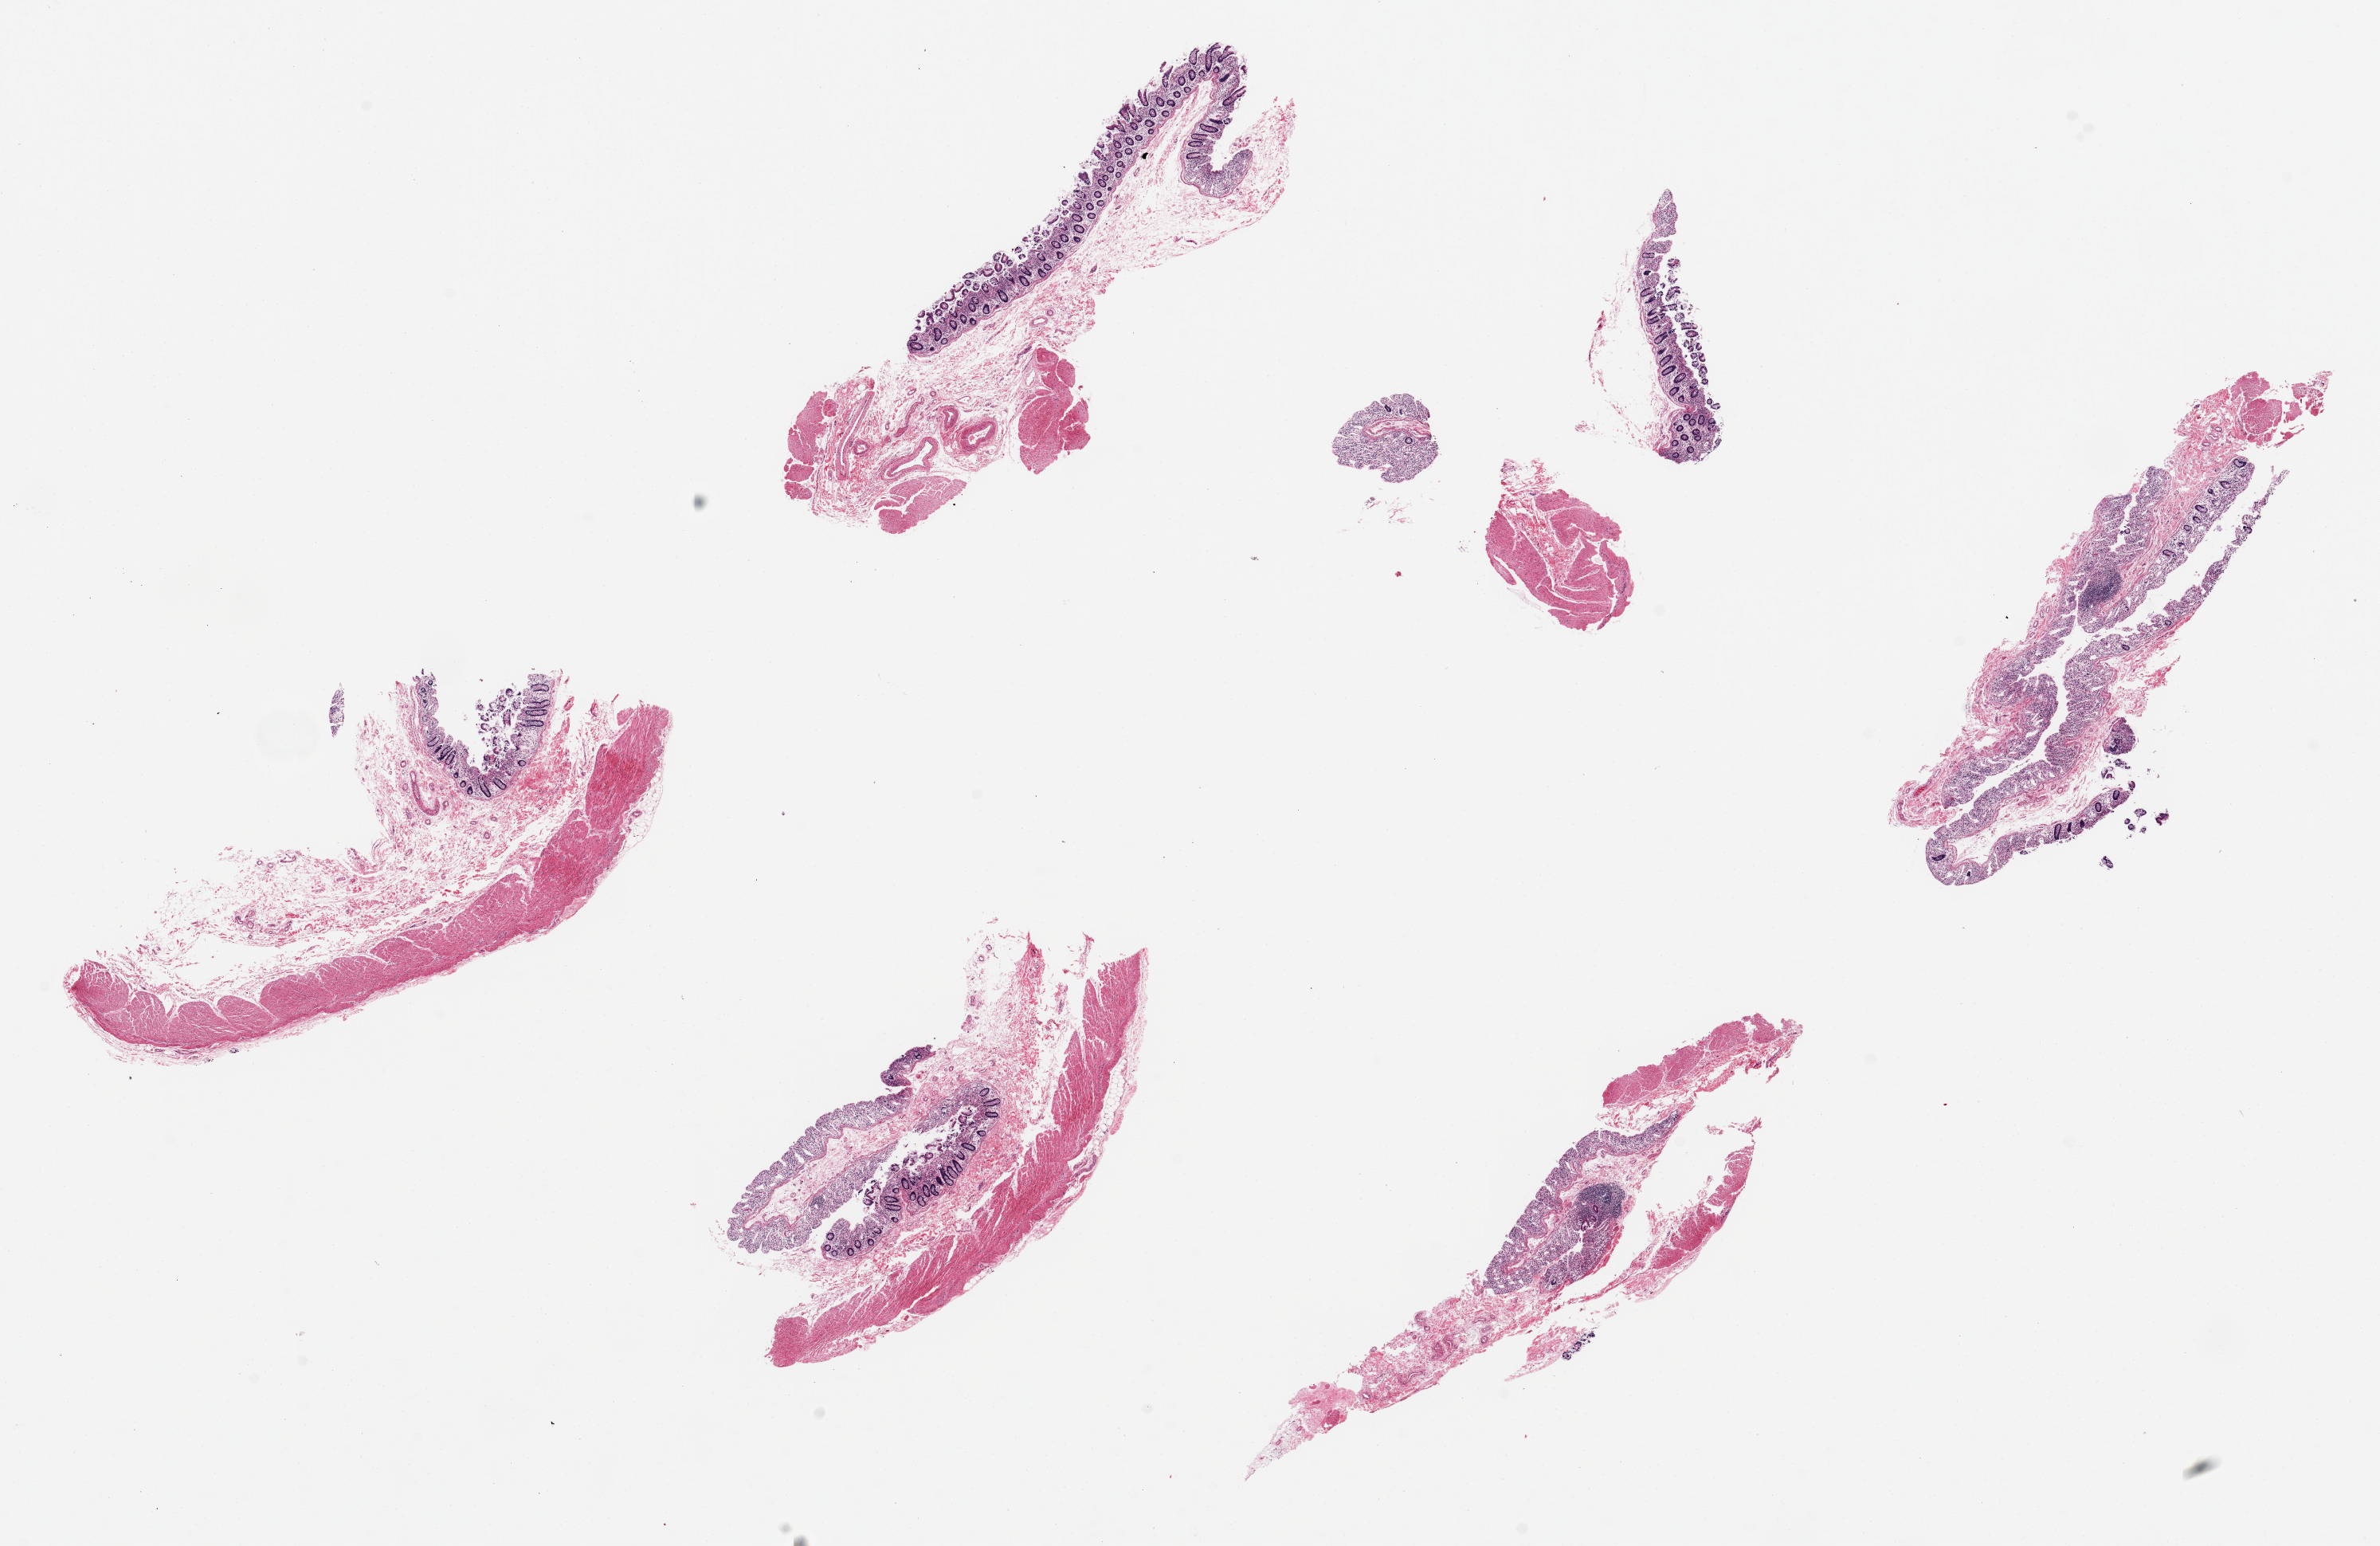
H&E whole-slide image — shown as a low-resolution overview of the whole scanned area (about 23.6 x 15.3 mm, slide scanned at 20x); PAXgene-fixed, paraffin-embedded tissue; sampled site (target tissue): transverse colon; donor tissue sample. Donor sex: male.
• review note (as recorded): 6 pieces up to 6x2.7 mm; patchy preserved mucosa, otherwise autolyzed; muscle slight autolysis